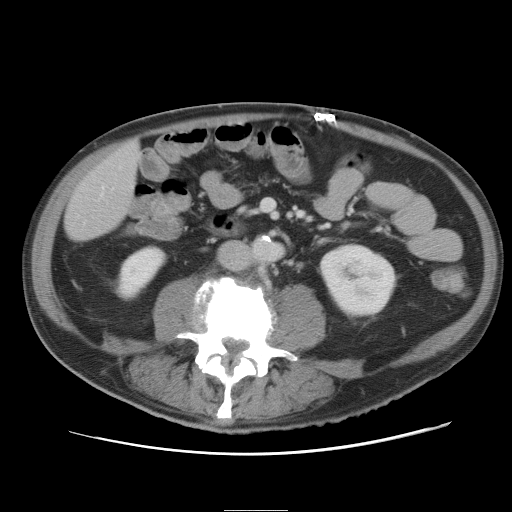
Contrast-enhanced abdominal CT, one axial slice; slice 6 of 89 in the series (ordered by position); intravenous contrast given; soft-tissue window (W 400 / L 40 HU); 5 mm slice thickness; 512 × 512 image matrix. Male patient, age 69 years. Case-level facts recorded for this patient, not image findings: diagnosis: colorectal cancer liver metastases, imaged before liver resection; multiple liver metastases: no; largest metastasis: 8.5 cm; disease in both lobes: no.
Structures marked on this image (expert manual segmentation):
- liver: bounding box (x1, y1, x2, y2) in pixels: (66, 141, 141, 240)
- planned liver remnant (the part of the liver to remain after resection): (66, 141, 140, 240)